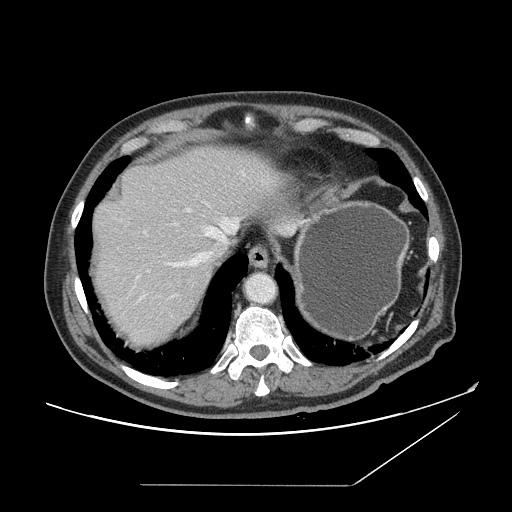
Contrast-enhanced abdominal CT, one axial slice; slice 129 of 166 in the series (ordered by position); soft-tissue window (W 400 / L 40 HU); 2.5 mm slice thickness; 512 × 512 image matrix, field of view 416 × 416 mm. Male patient, age 80 years. Case-level facts recorded for this patient, not image findings: diagnosis: colorectal cancer liver metastases, imaged before liver resection; multiple liver metastases: no; largest metastasis: 2.2 cm.
Outlined on this slice (outlined manually by an expert reader):
- hepatic veins: bounding box [x1, y1, x2, y2] px = [166, 217, 239, 268]
- liver: [92, 144, 285, 345]
- planned liver remnant (the part of the liver to remain after resection): [92, 145, 284, 256]
- portal vein (with intrahepatic branches): [144, 210, 191, 233]